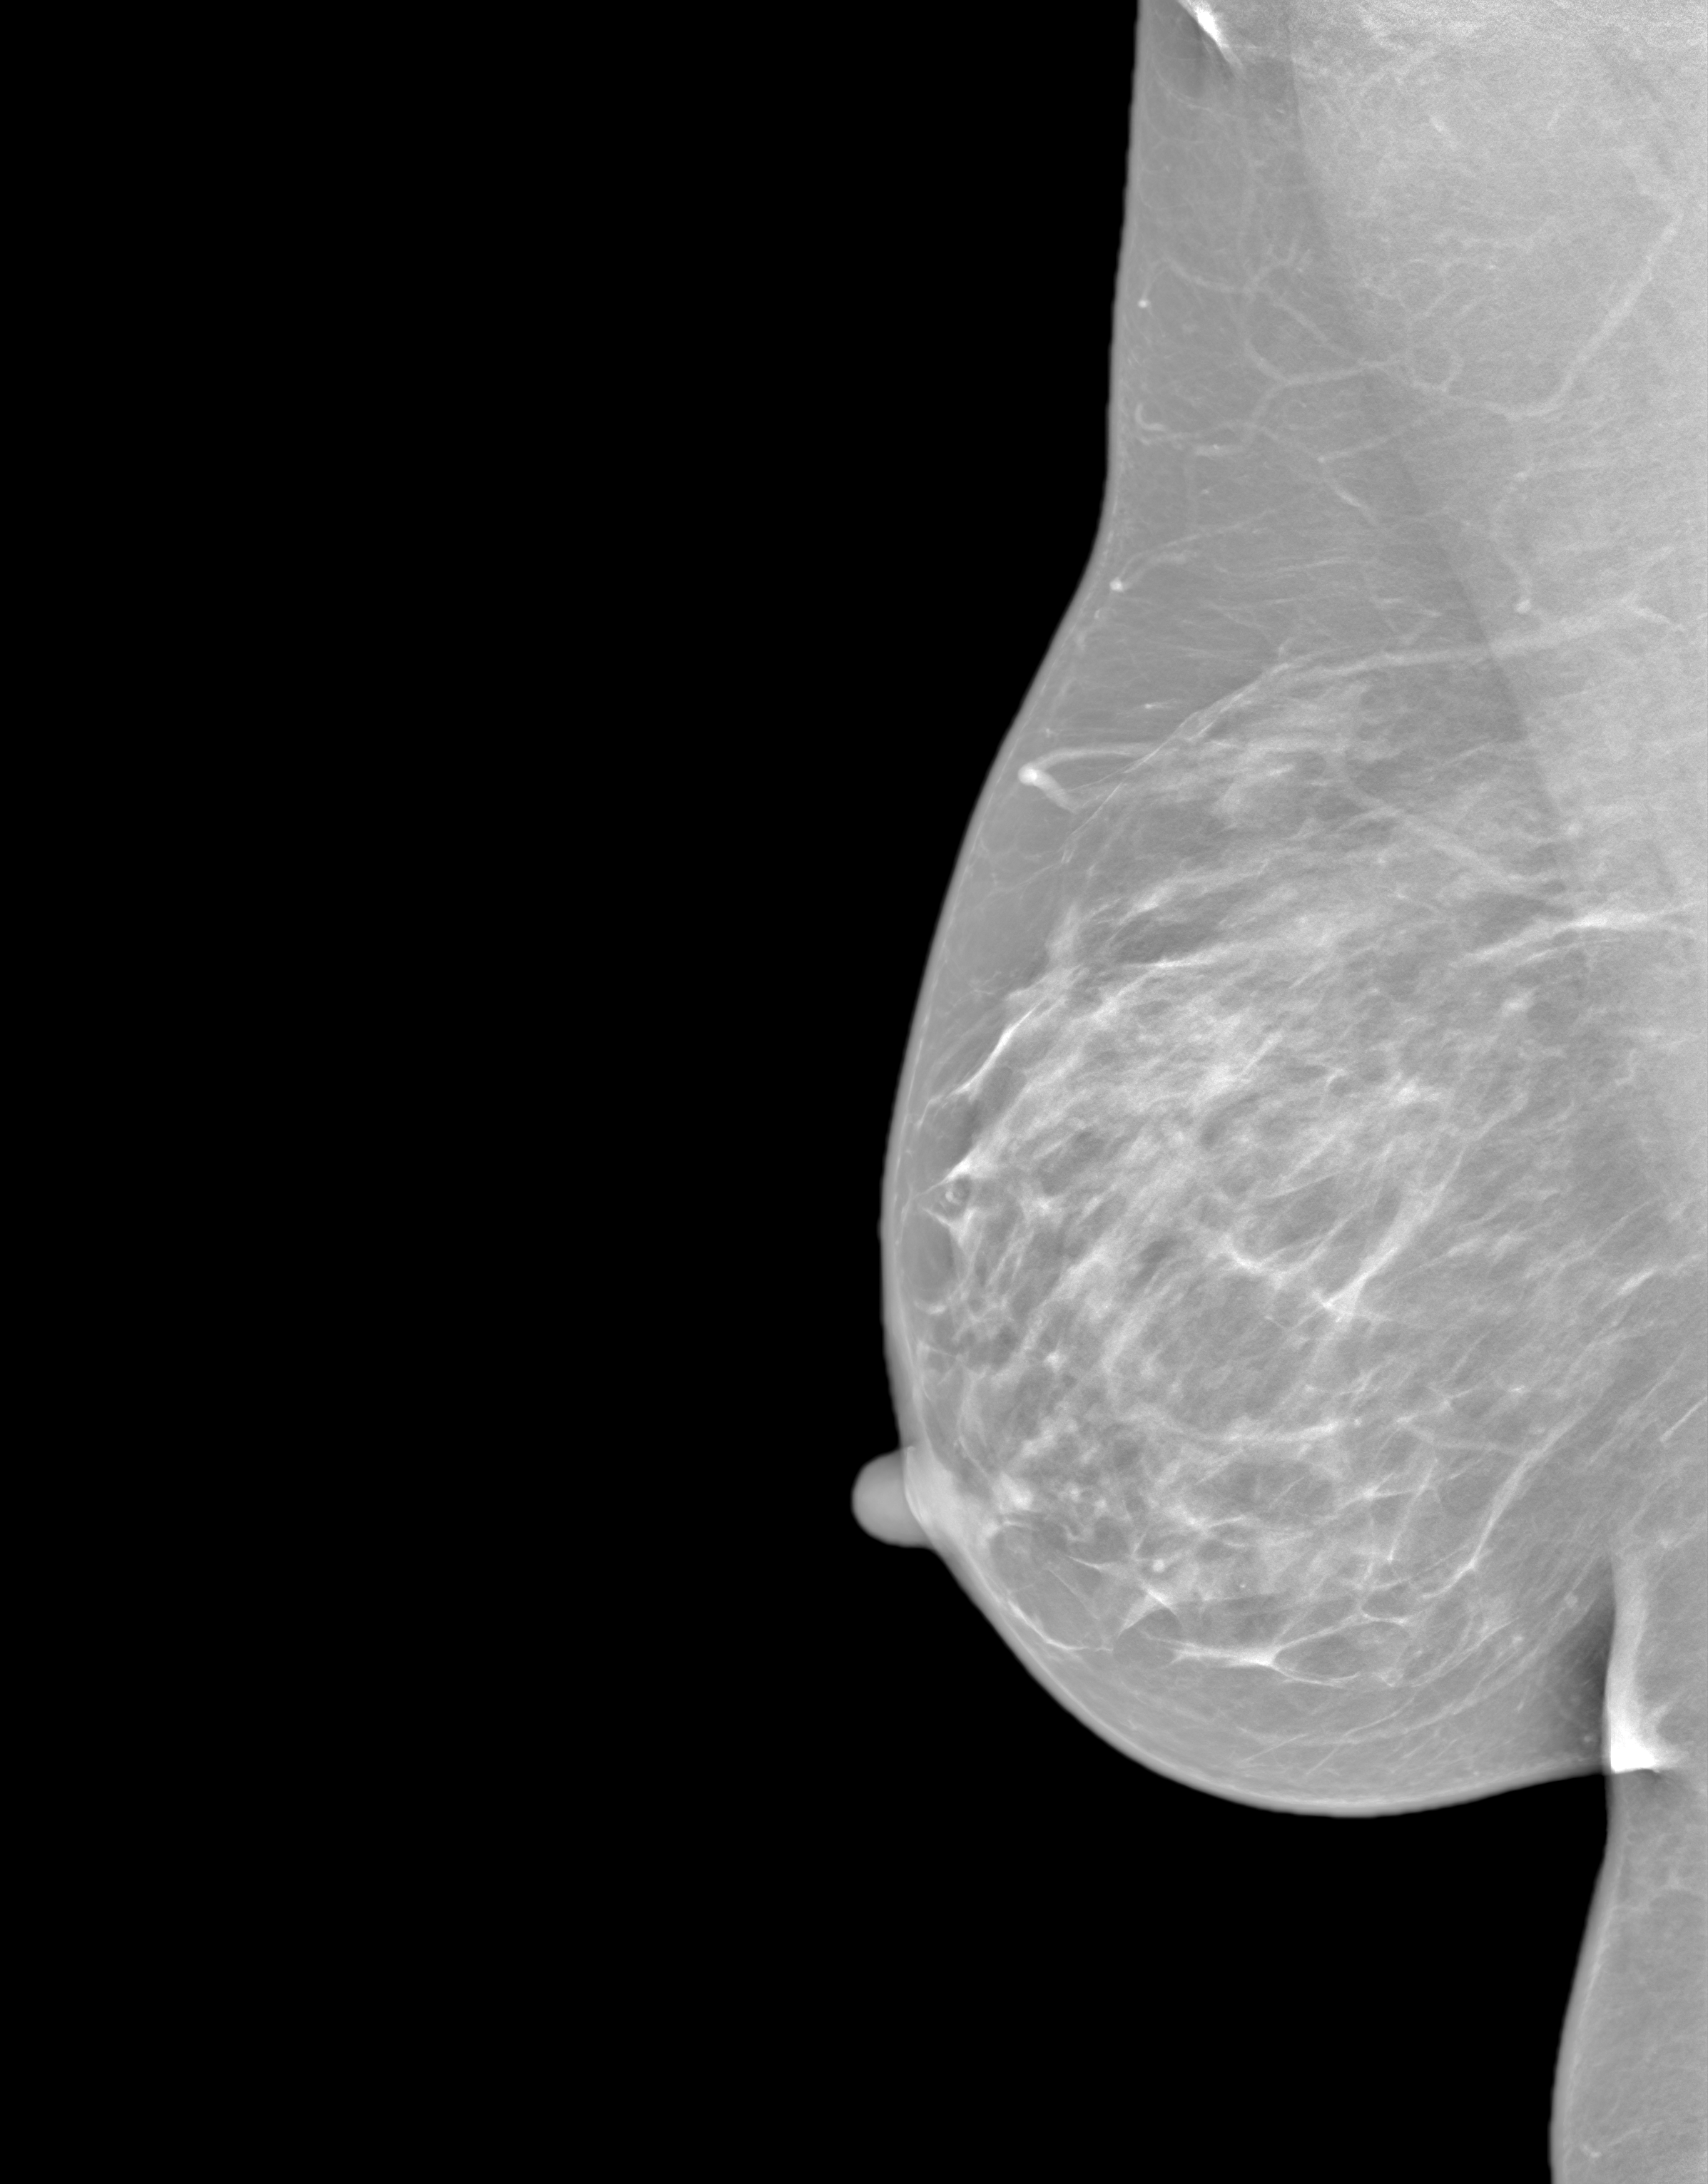
Annual screening mammography examination. Patient aged 50 years (female).
Image type: synthesized 2-D view from tomosynthesis. Breast: right. Projection: mediolateral oblique (MLO) view.